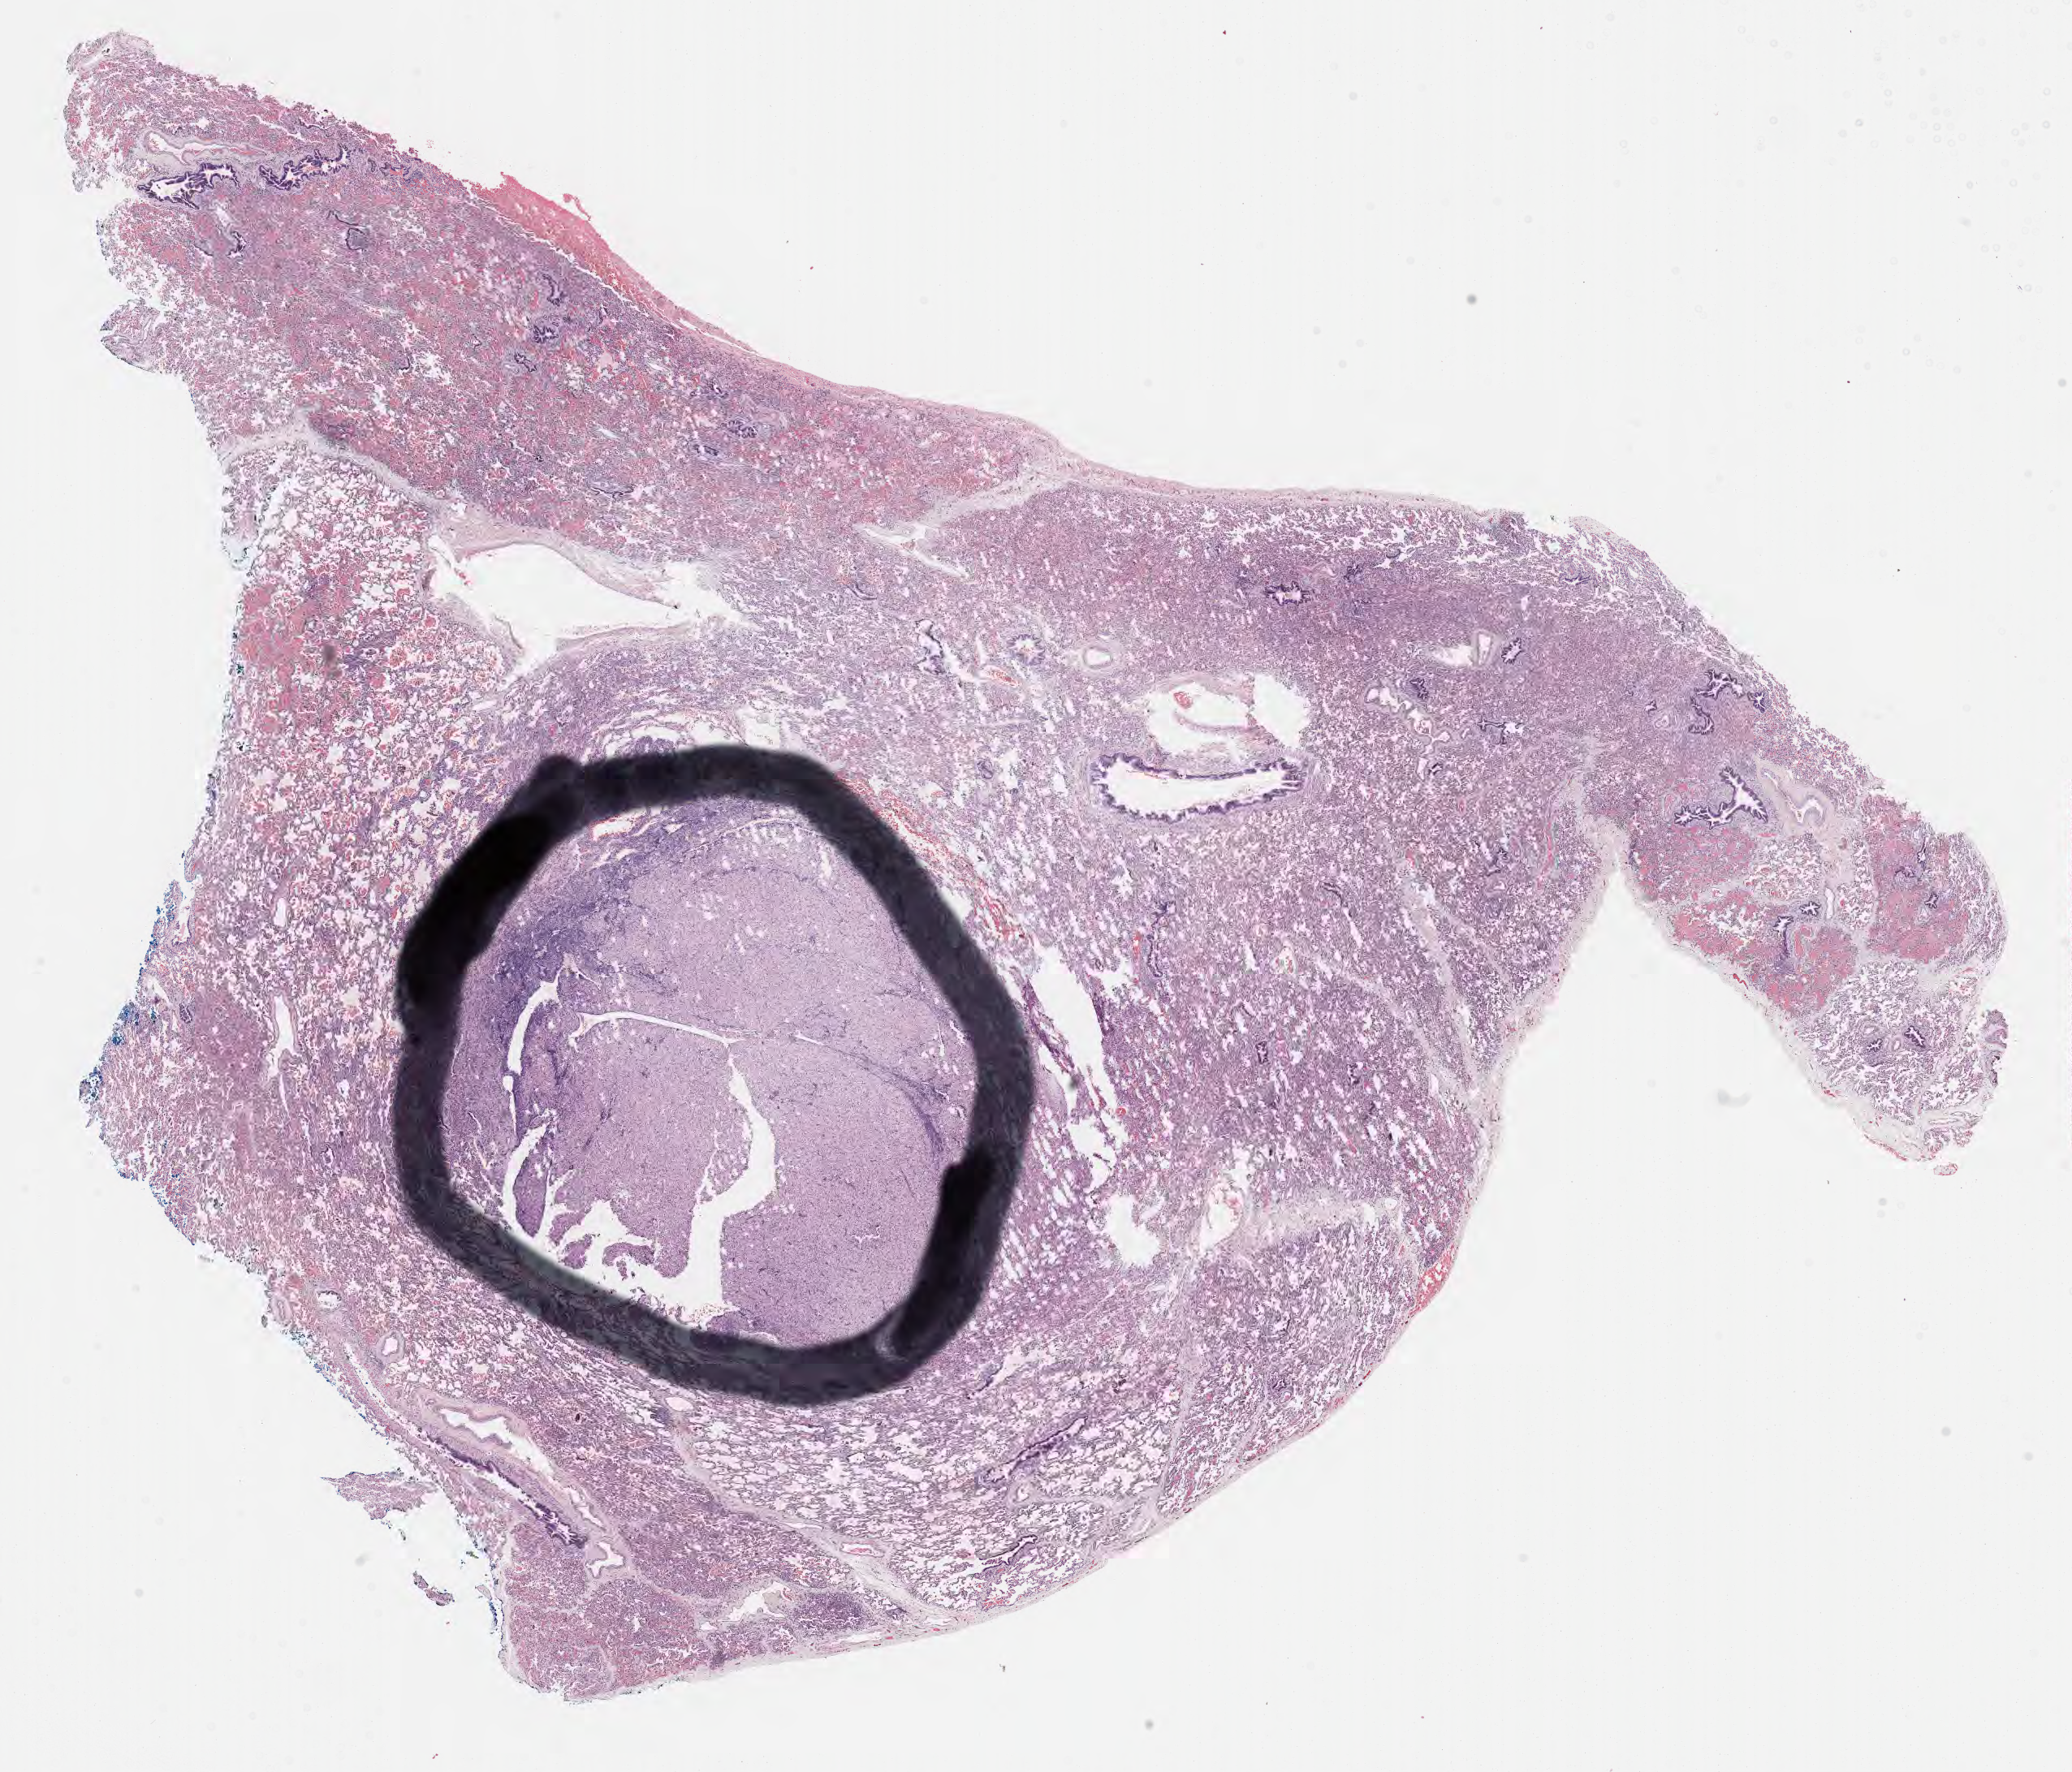
Whole-slide image, H&E stain — a low-resolution overview of the entire scanned area, about 20.6 x 17.7 mm, formalin-fixed, paraffin-embedded (FFPE) tissue, metastatic tumor tissue, resected from lung. Male, age 2 years at initial diagnosis. Pathologist review of this section (percent, as recorded): tumor cells 96%, tumor nuclei 94%.
Patient diagnosis (primary): Nephroblastoma, NOS.